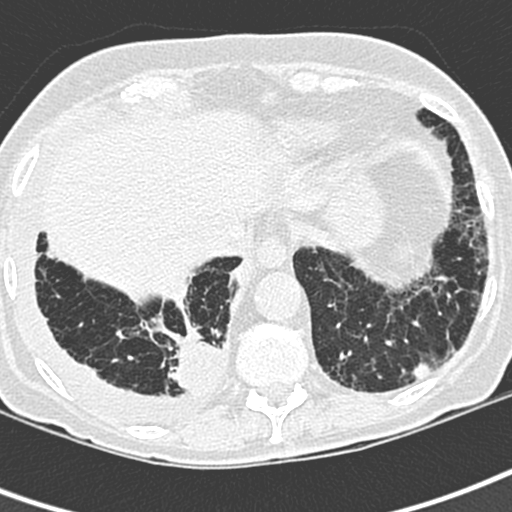
Low-dose screening chest CT, one axial slice. Position 67 of 220 along the scan axis. 120 kVp. Lung window (W 1500 / L -600 HU). 1.3 mm slice thickness. 512 × 512 image matrix, field of view 288 × 288 mm.
Annotated regions visible in this slice (outlined manually by an expert reader):
- lesion 1 (tumor, lower lobe of right lung): bounding box <168,330,222,393> (left, top, right, bottom; pixels)
- lesion 2 (nodule, lower lobe of left lung): <414,363,431,377>